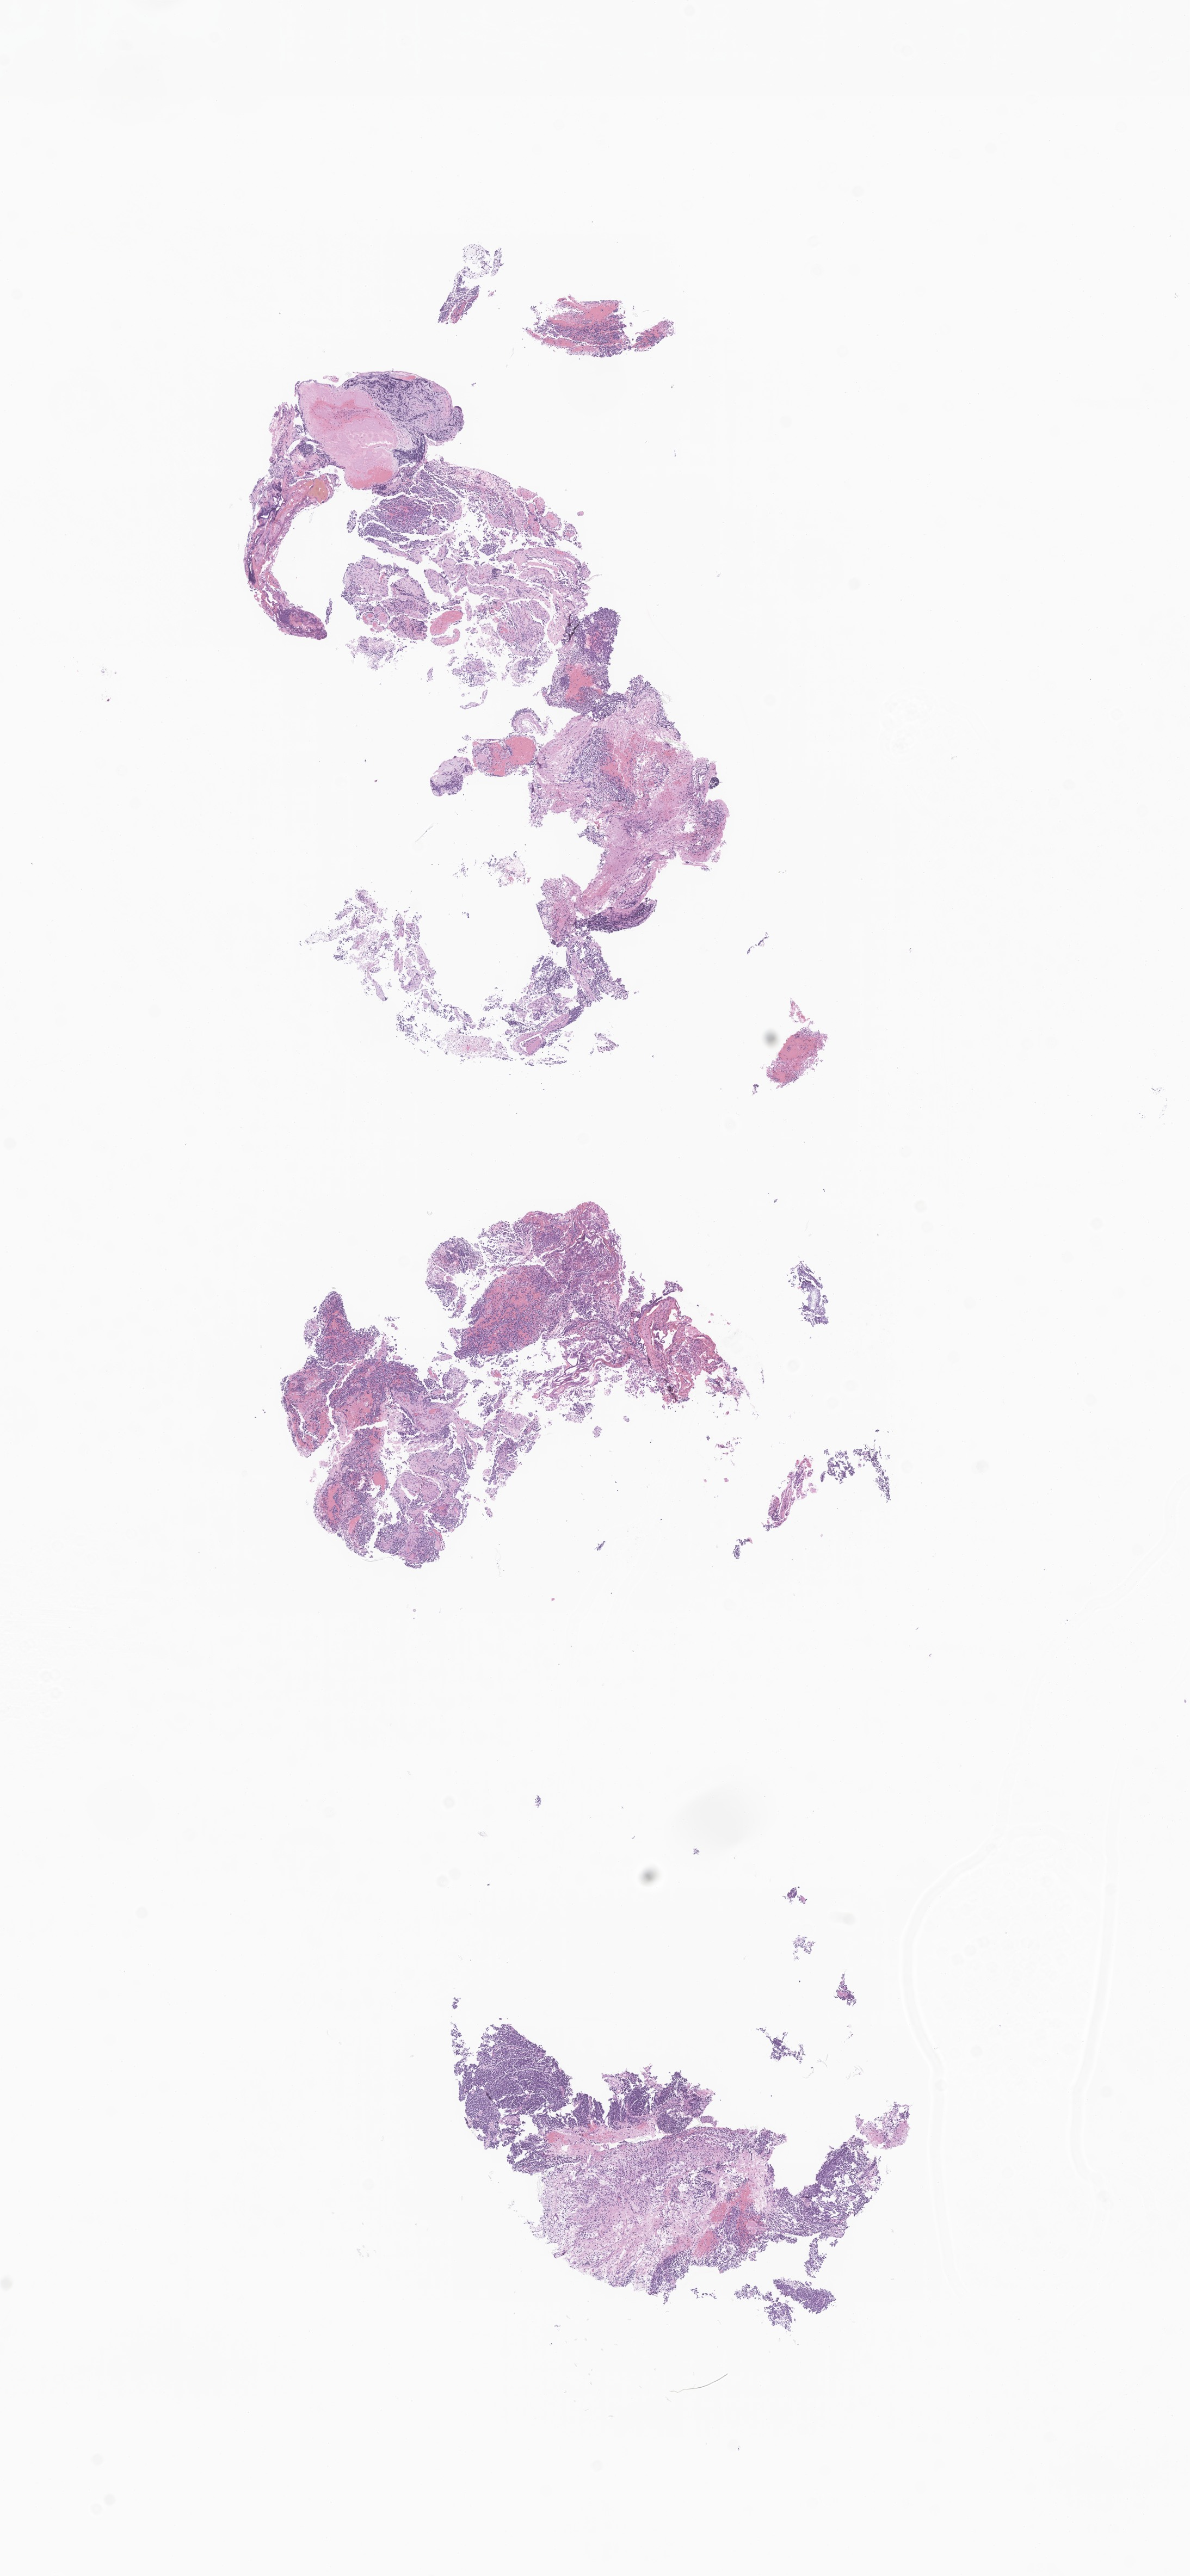
Whole-slide image, H&E stain of tumor tissue from the brain, low-resolution overview of the scanned area, about 9.2 x 20.0 mm. Formalin-fixed, paraffin-embedded (FFPE) tissue. Patient: male, age 87 months (7 years 3 months).
Recorded diagnosis: Medulloblastoma, NOS.